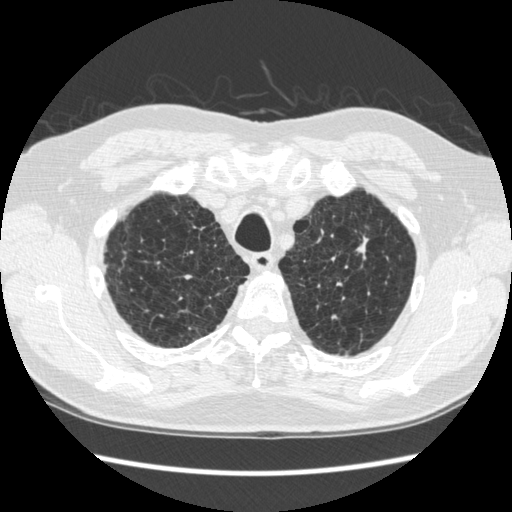
Chest CT (low-dose screening protocol), one axial image. Second annual screen. Lung window (W 1500 / L -600 HU). 120 kVp. Slice 49 of 295 in the series. Male participant, aged 70 years at enrolment. Former smoker at enrolment.
Lesion marked by an expert reader, bounding box <332,216,393,283> (left, top, right, bottom; pixels). The screening reader recorded 5 non-calcified nodules or masses ≥4 mm on this exam (right lower lobe, right lower lobe, right lower lobe, left upper lobe, left lower lobe); which of them this box marks is not recorded. Official screen result: positive, change unspecified: nodule(s) >= 4 mm or enlarging nodule(s), mass(es), or other non-specific abnormalities suspicious for lung cancer. Participant outcome: lung cancer diagnosed 479 days after this screen (after the third annual screen) — squamous cell carcinoma, NOS, left upper lobe, moderately differentiated (G2), stage IA (AJCC 6th edition), 18 mm at pathology.